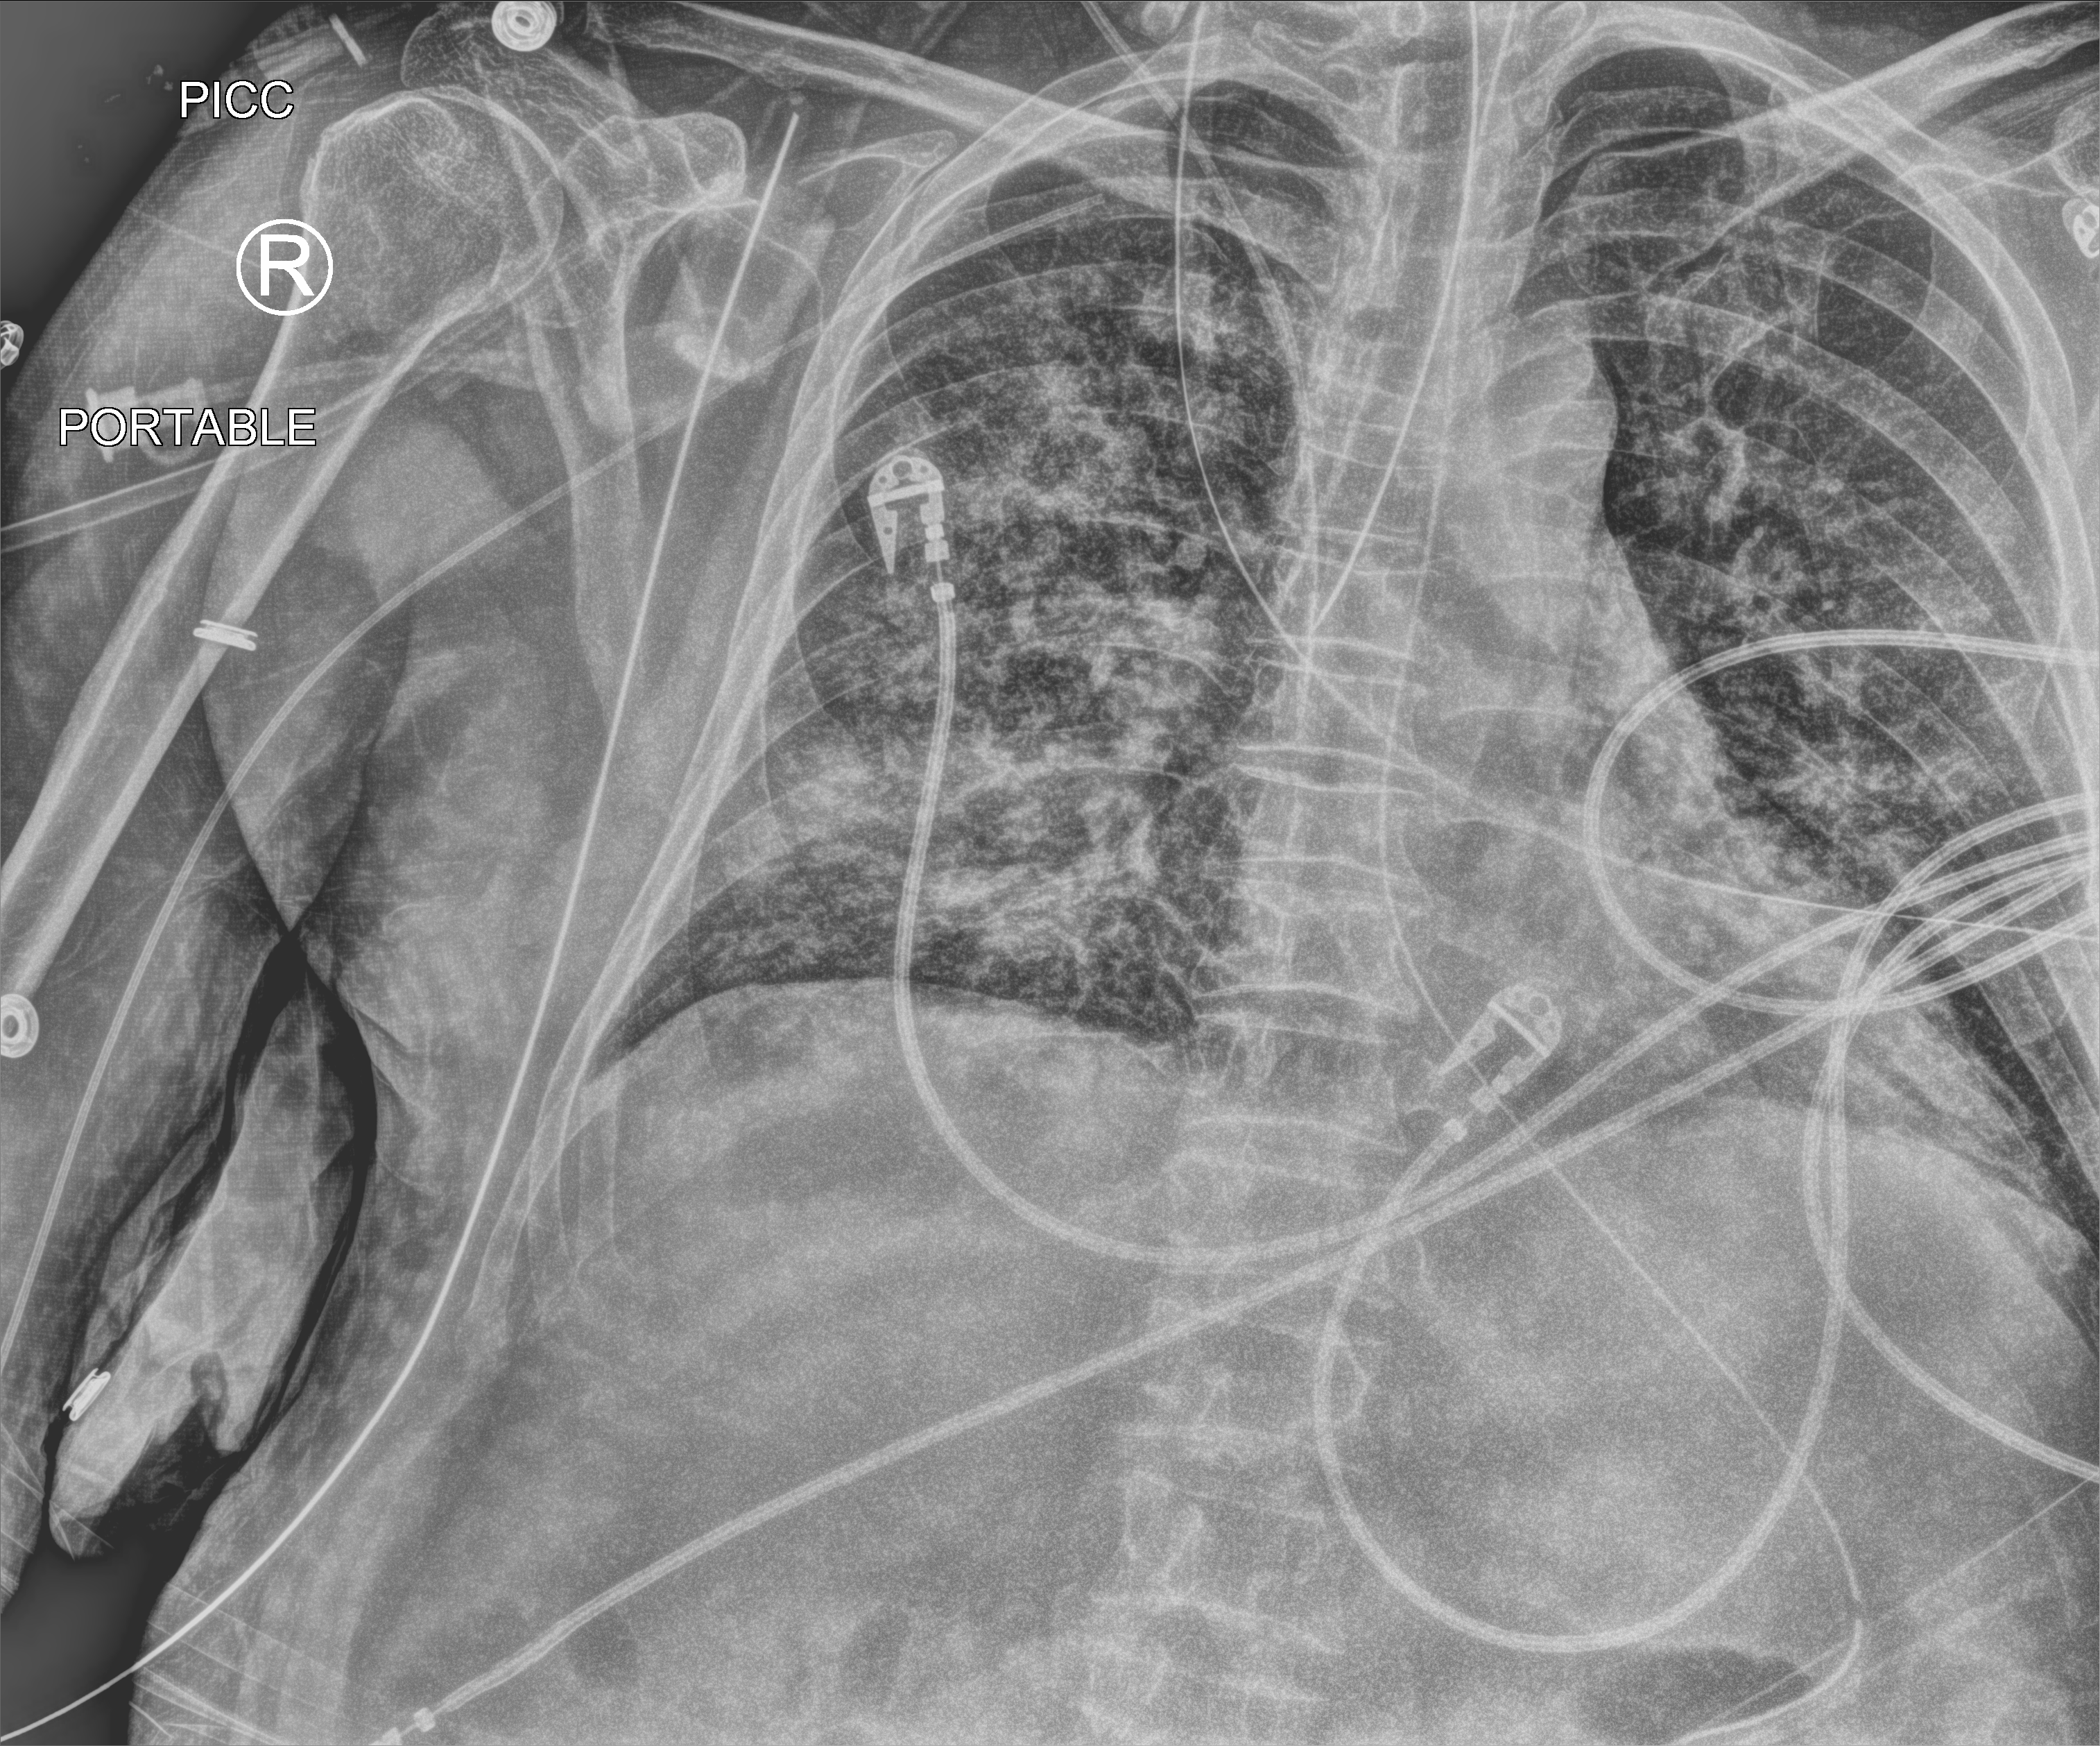
Portable chest radiograph, anteroposterior (AP) projection. Male patient hospitalised with COVID-19, age 60–74 years.
Admission-level facts for this patient (not findings on this image; timing relative to this image not recorded): mechanically ventilated during this hospital stay: yes; chronic kidney disease (admission record): no; admitted to intensive care during this hospital stay: yes.